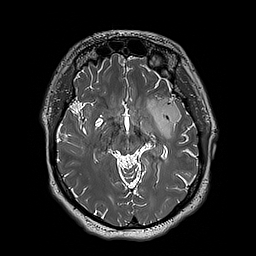
Brain MRI from a brain-tumour surgery series, one axial slice. Position 112 of 192 along the scan axis. 1 mm slice thickness. 256 × 256 image matrix, field of view 250 × 250 mm. Case-level facts recorded for this patient, not image findings: histopathology: Astrocytoma; WHO grade: 3; IDH mutation: yes; tumour location: Left Insular.
Structures marked on this image (manually delineated by an expert):
- tumour: bounding box (x1, y1, x2, y2) in pixels: (148, 98, 181, 139)